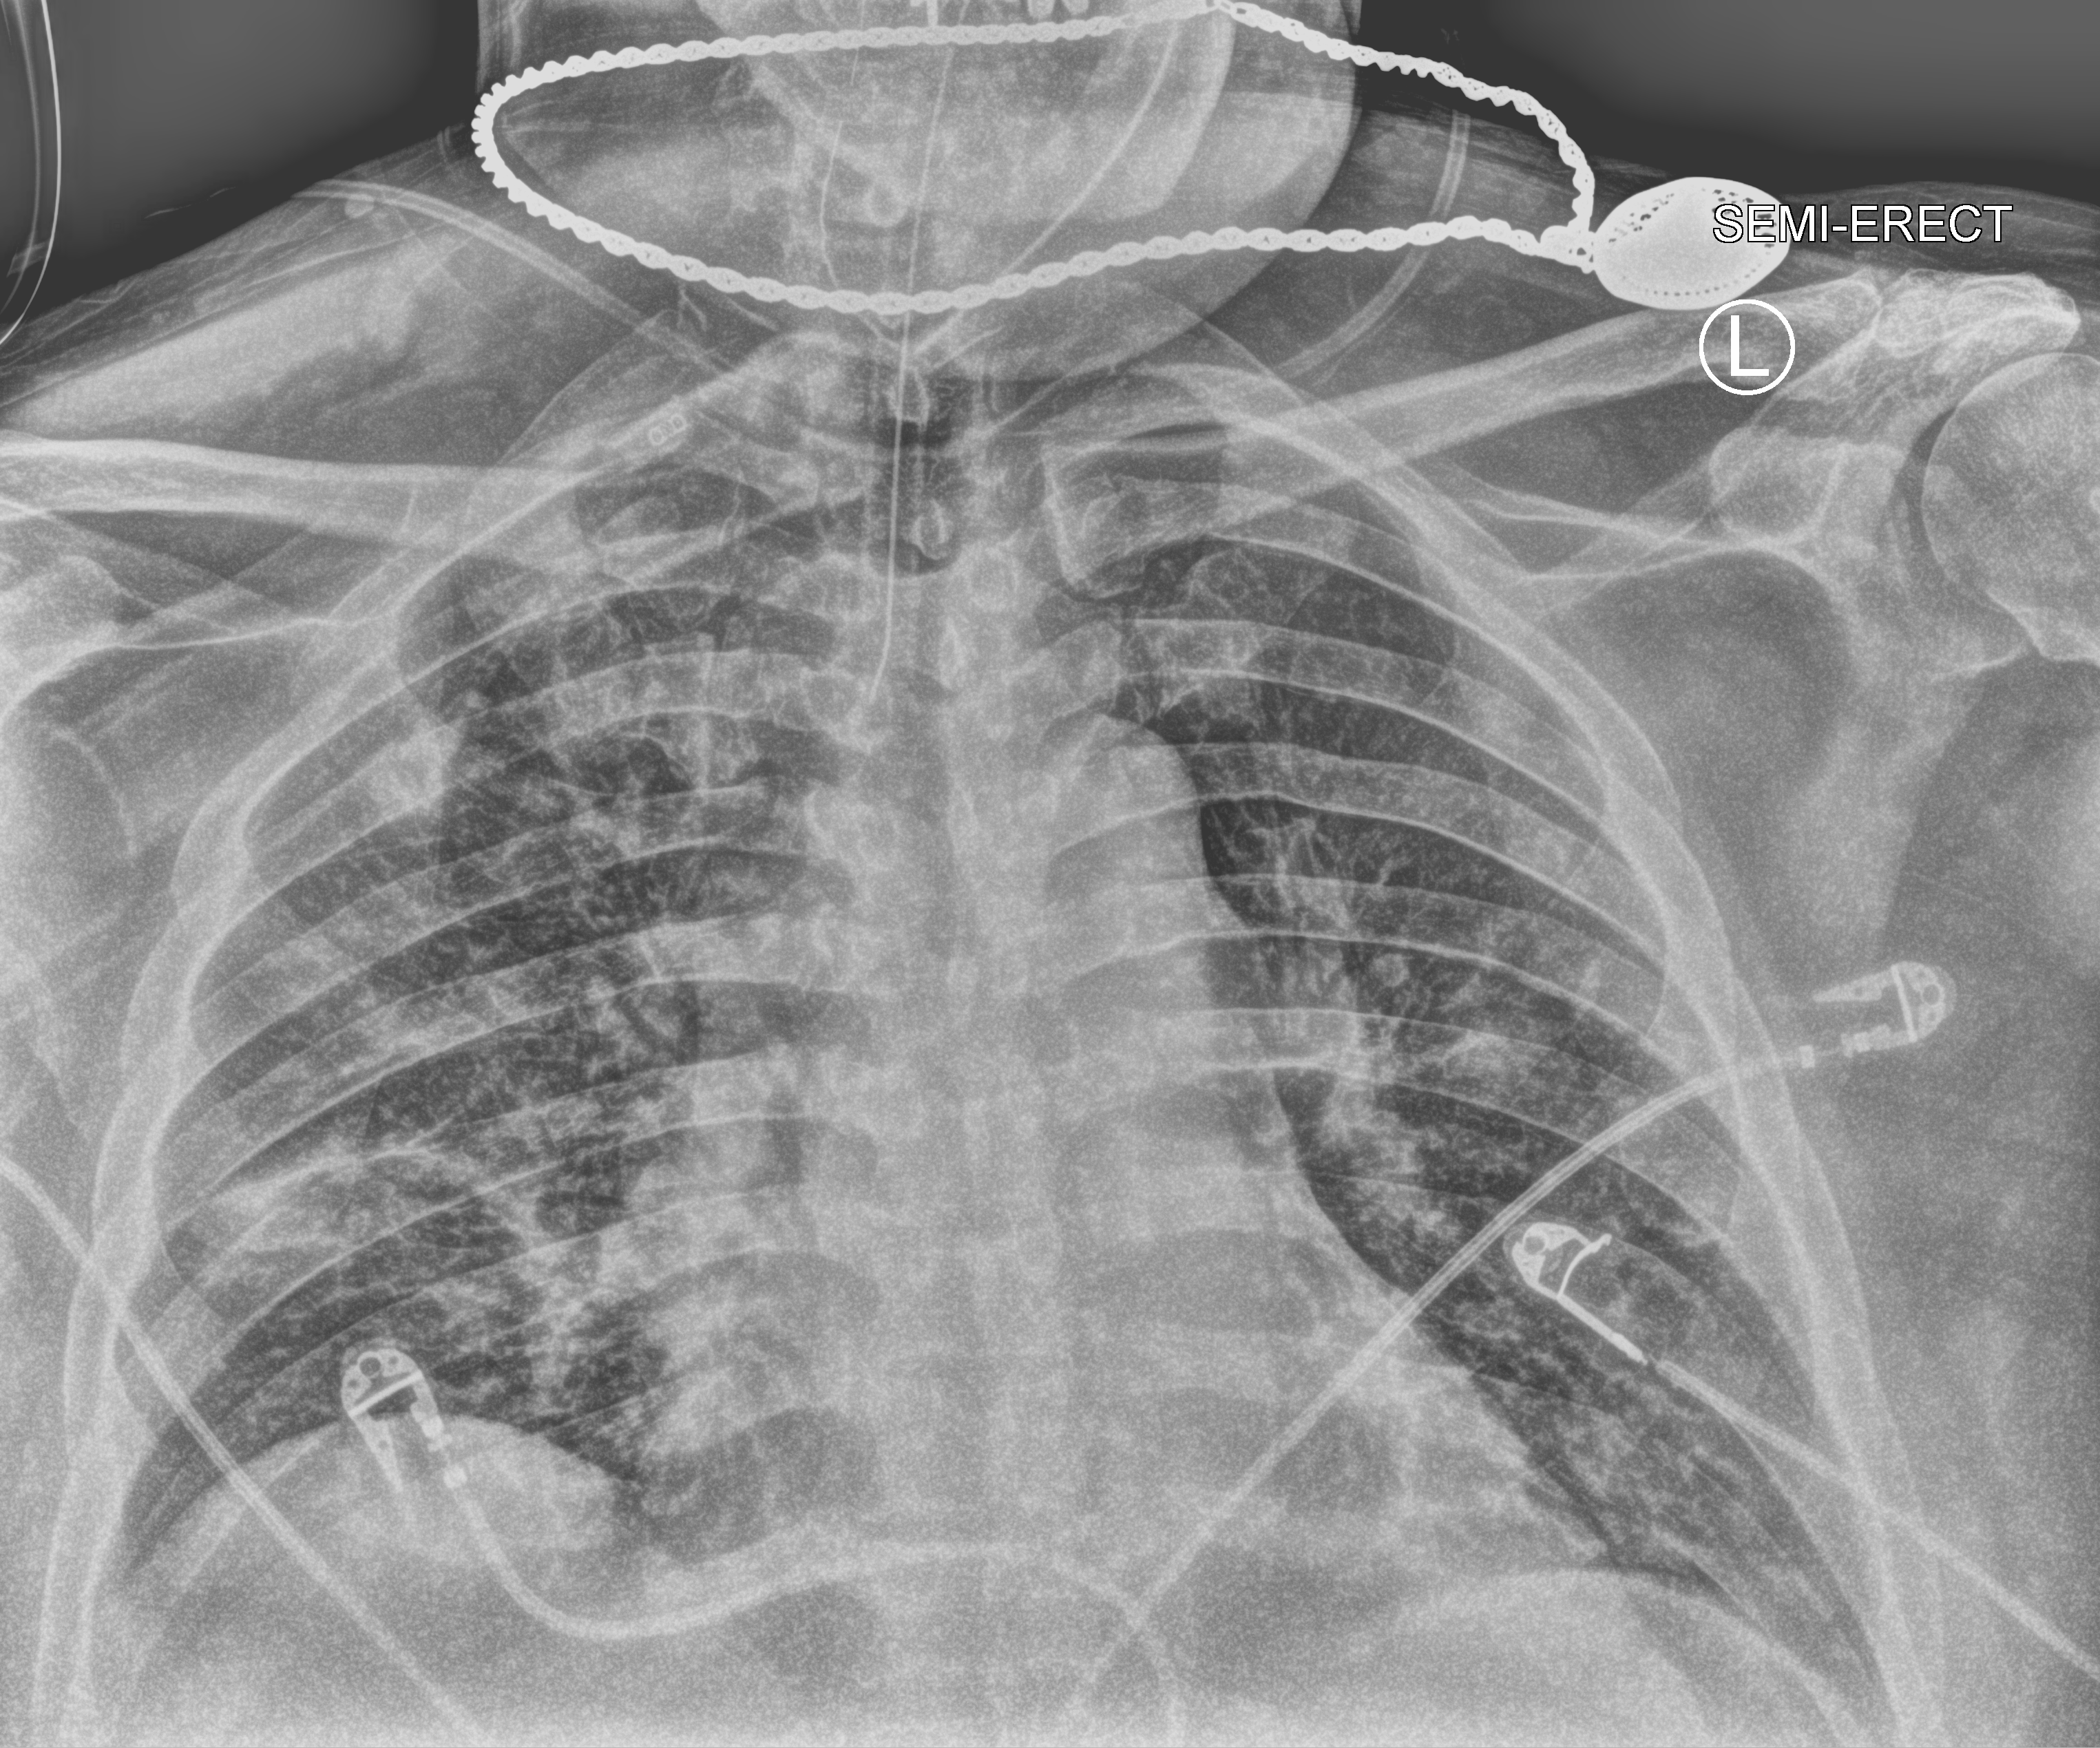
Bedside chest radiograph (computed radiography), anteroposterior (AP) projection. Male patient hospitalised with COVID-19, age 60–74 years.
Admission-level facts for this patient (not findings on this image; timing relative to this image not recorded):
- hypertension (admission record): yes
- admitted to intensive care during this hospital stay: no
- mechanically ventilated during this hospital stay: no